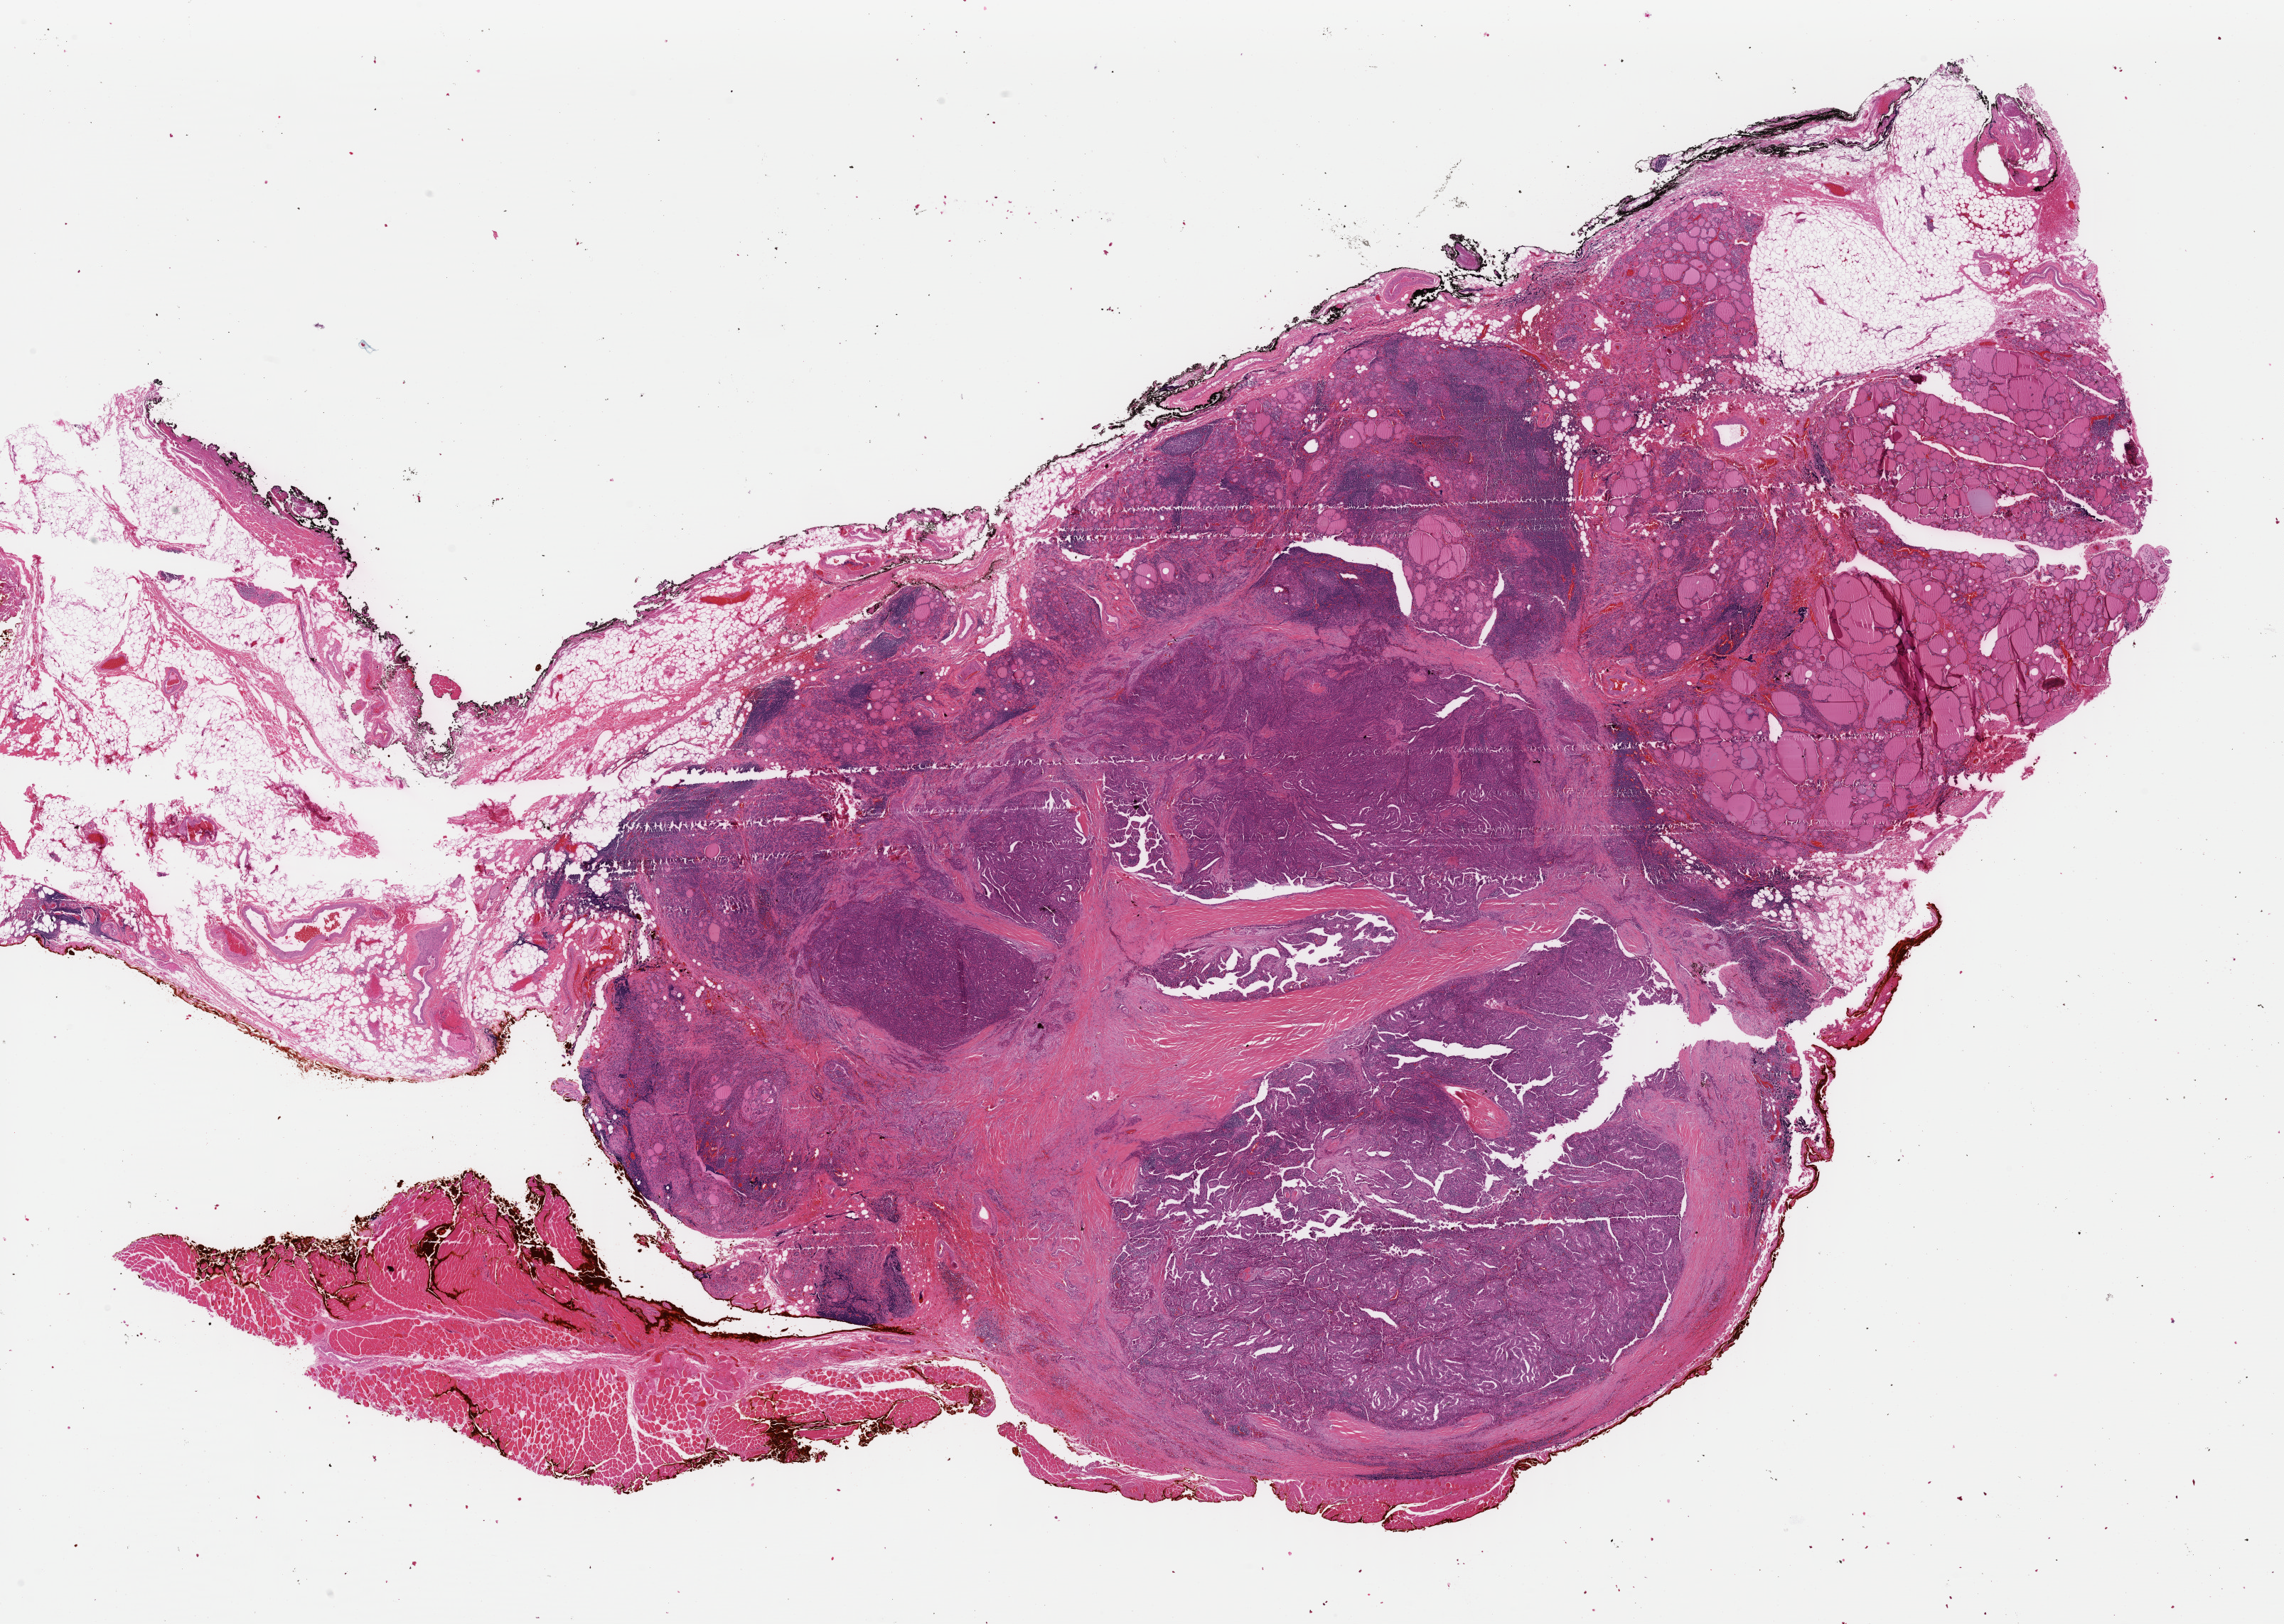
Digitized H&E-stained tissue section (whole slide), low-resolution overview of the scanned area, about 25.3 x 18.0 mm (acquisition: 40x scan), formalin-fixed paraffin-embedded (FFPE) diagnostic section, sample: primary tumour, thyroid. Female, age 51 years at initial diagnosis.
Diagnosis: Papillary carcinoma, columnar cell.